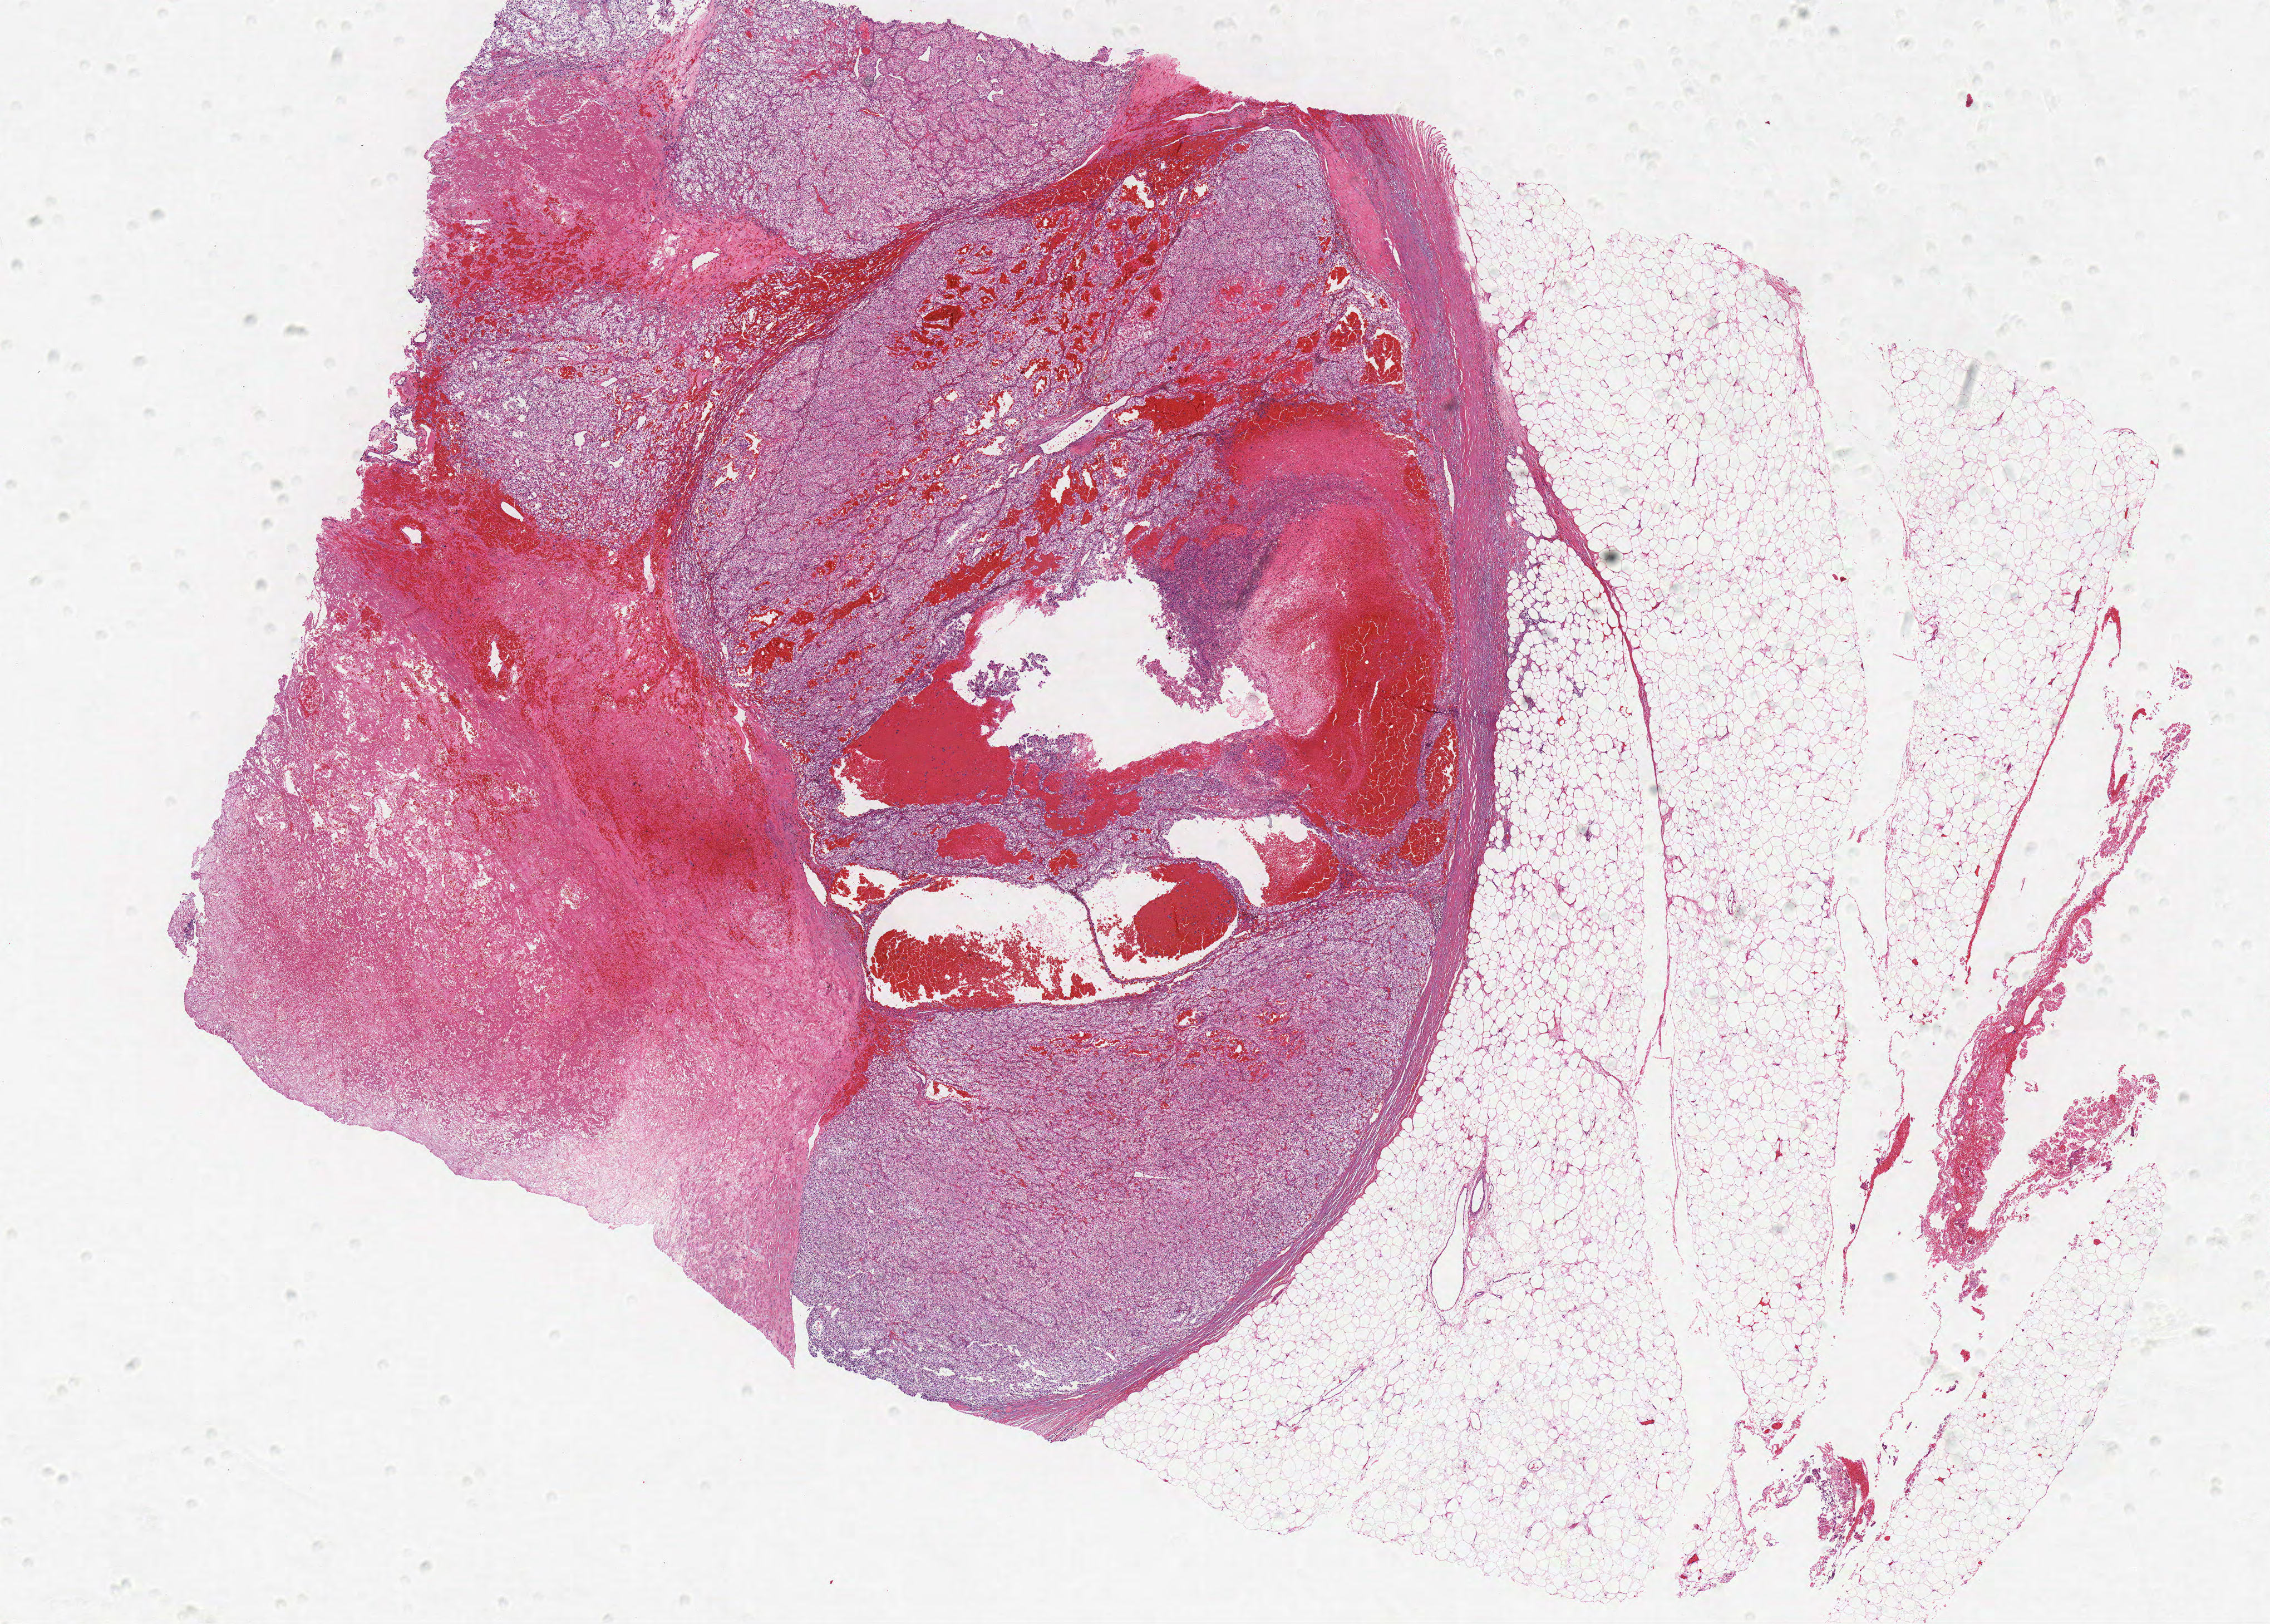
Hematoxylin and eosin (H&E) stained whole-slide image — a low-resolution overview of the entire scanned area, about 16.3 x 11.7 mm. FFPE section. Primary tumour sample from the kidney. Patient: male, age at initial diagnosis 57 years. Histologic grade: G3 (poorly differentiated).
Laterality: left. Pathologic diagnosis: Clear cell adenocarcinoma, NOS. AJCC pathologic stage: III.